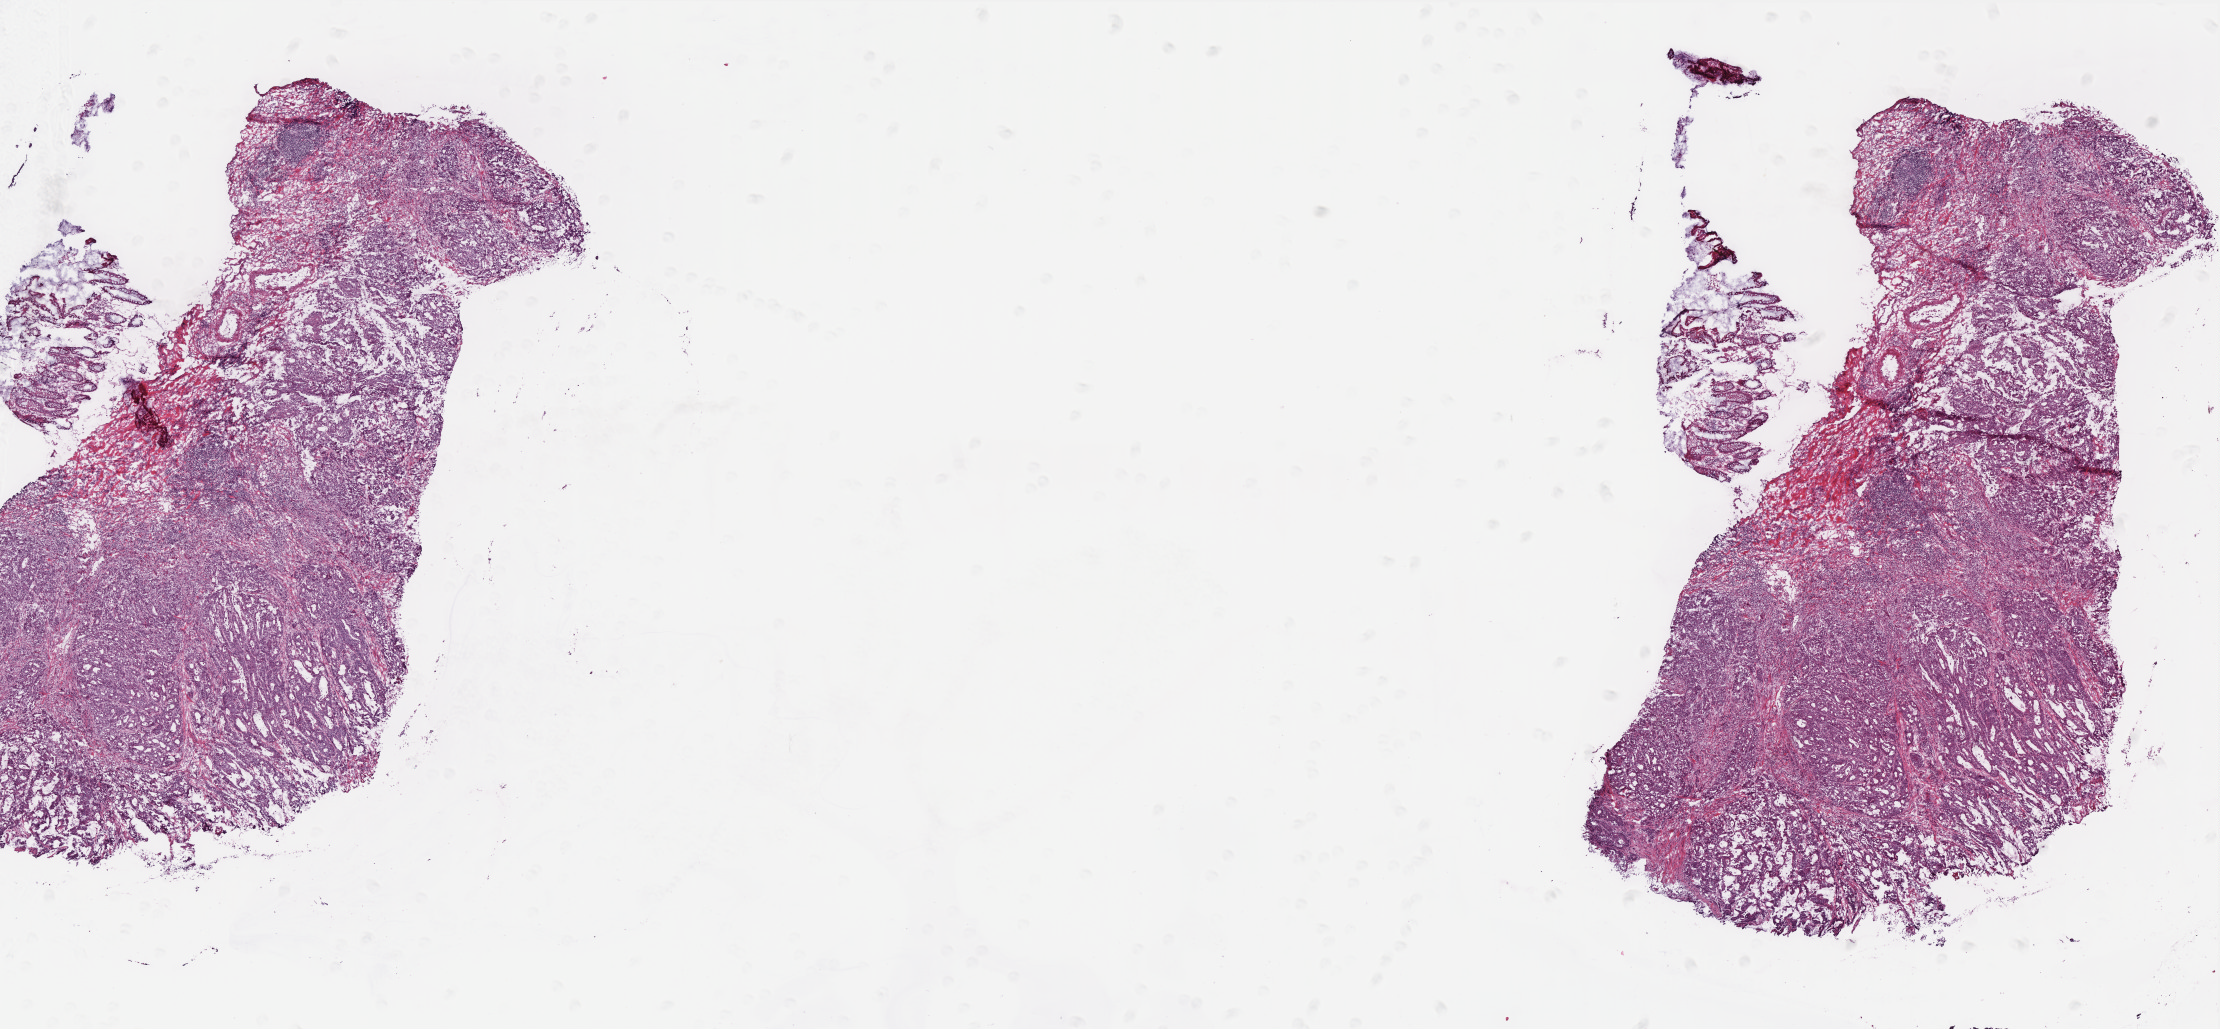
Whole-slide histology image, Hematoxylin and eosin (H&E) stained — low-resolution overview of the scanned area, about 17.8 x 8.2 mm; frozen section from the top of the tissue portion; colon, primary tumour sample. Male patient; age at initial diagnosis 64 years. Pathologist review of this section (percent, as recorded): tumour cells 70%, tumour nuclei 70%, normal cells 10%, stromal cells 19%, necrosis 1%. Inflammatory infiltration, as recorded: lymphocyte infiltration 8%, monocyte infiltration 6%, neutrophil infiltration 8%.
Lymph nodes positive (case pathology): 0 of 41 examined. Pathologic diagnosis: Adenocarcinoma, NOS (ascending colon). AJCC pathologic stage: IIA (6th edition).